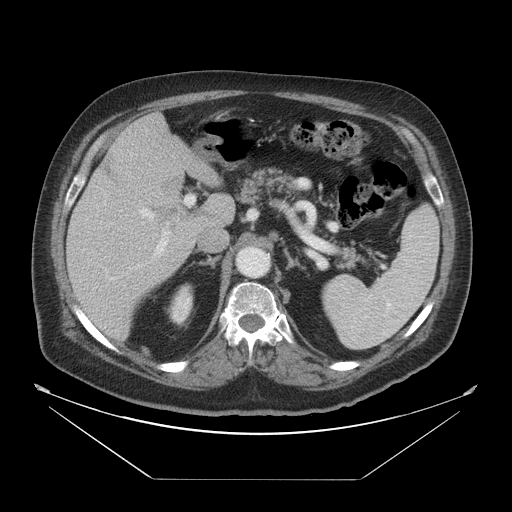
Contrast-enhanced abdominal CT, one axial slice; slice 31 of 45 in the series (ordered by position); 120 kVp; intravenous contrast given; soft-tissue window (W 400 / L 40 HU); 512 × 512 image matrix. Male patient, age 87 years. Case-level facts recorded for this patient, not image findings: diagnosis: colorectal cancer liver metastases, imaged before liver resection; multiple liver metastases: no; largest metastasis: 4.5 cm; disease in both lobes: yes.
Annotated regions visible in this slice (outlined manually by an expert reader):
- liver: bounding box [x1, y1, x2, y2] px = [66, 113, 227, 342]
- planned liver remnant (the part of the liver to remain after resection): [119, 113, 208, 170]
- portal vein (with intrahepatic branches): [120, 196, 228, 267]
- liver metastasis: [160, 172, 183, 197]
- liver metastasis: [98, 148, 124, 186]